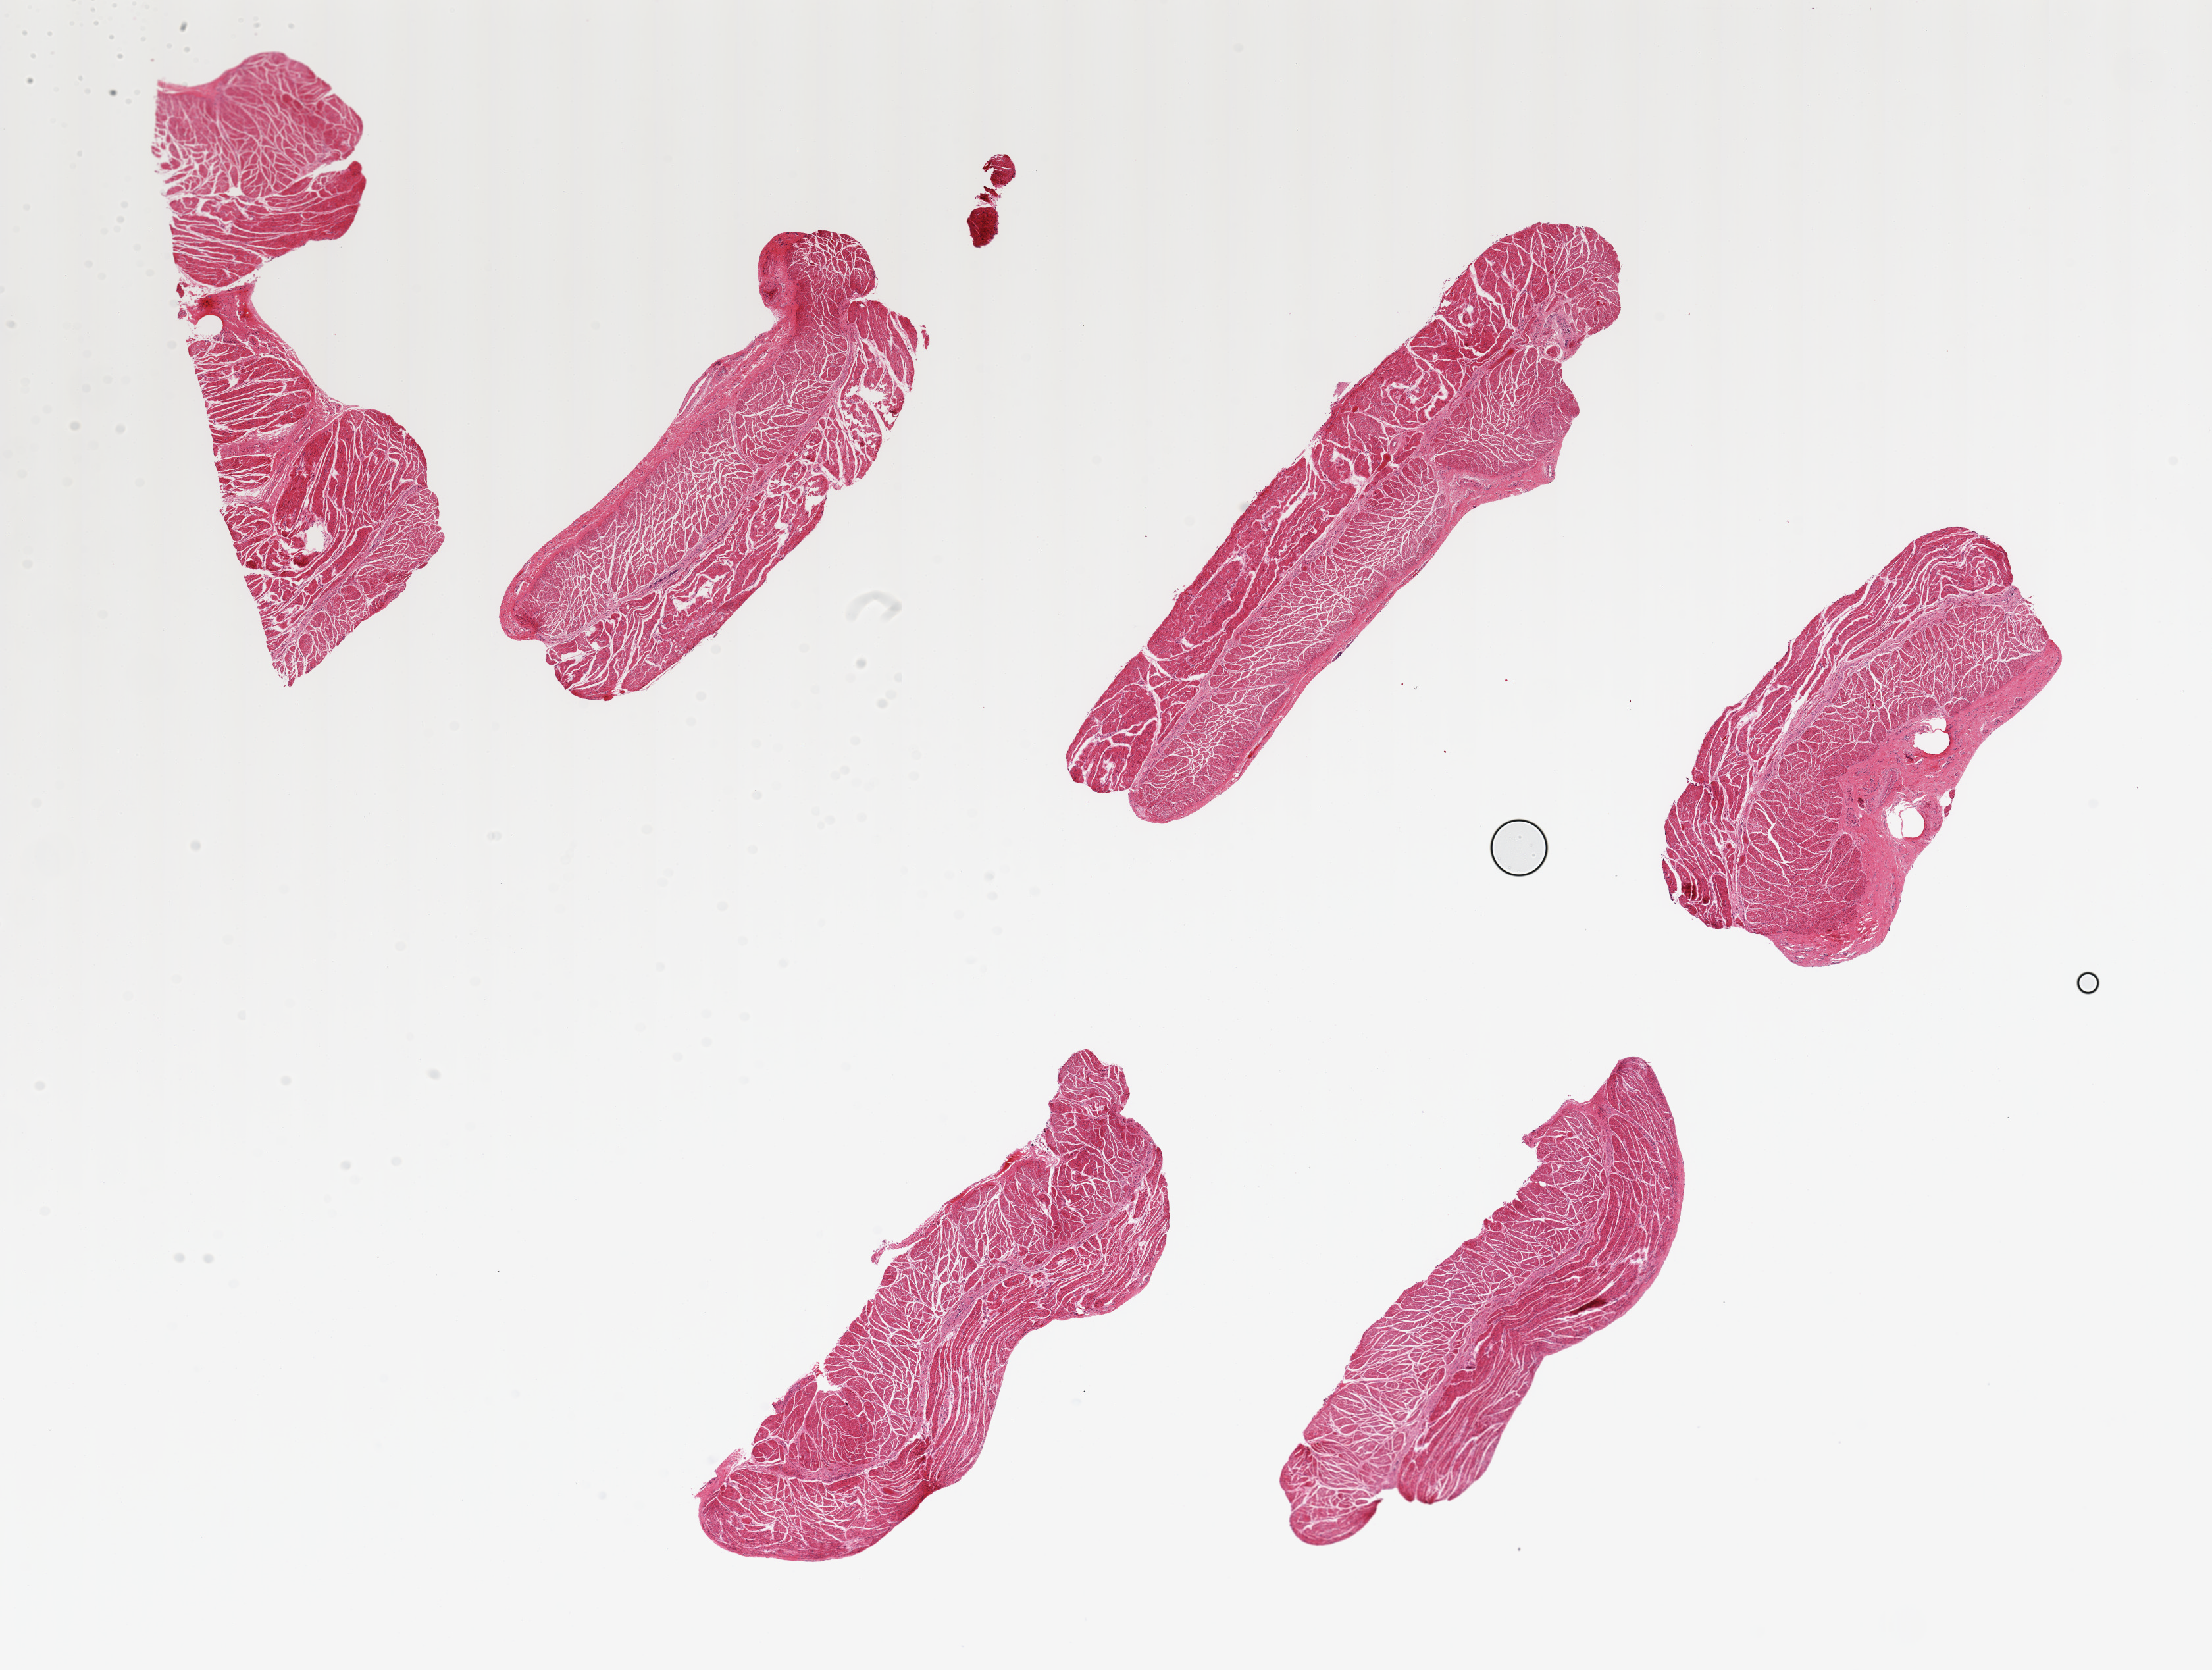
Haematoxylin and eosin whole-slide image — whole scanned area (about 26.6 x 20.1 mm) shown as a low-resolution overview, PAXgene-fixed paraffin-embedded (PFPE) section, sampled site (target tissue): esophageal muscle, donor tissue sample. Female donor.
Reviewer comment on this tissue sample: 6 pieces ~8x2mm, all muscle.